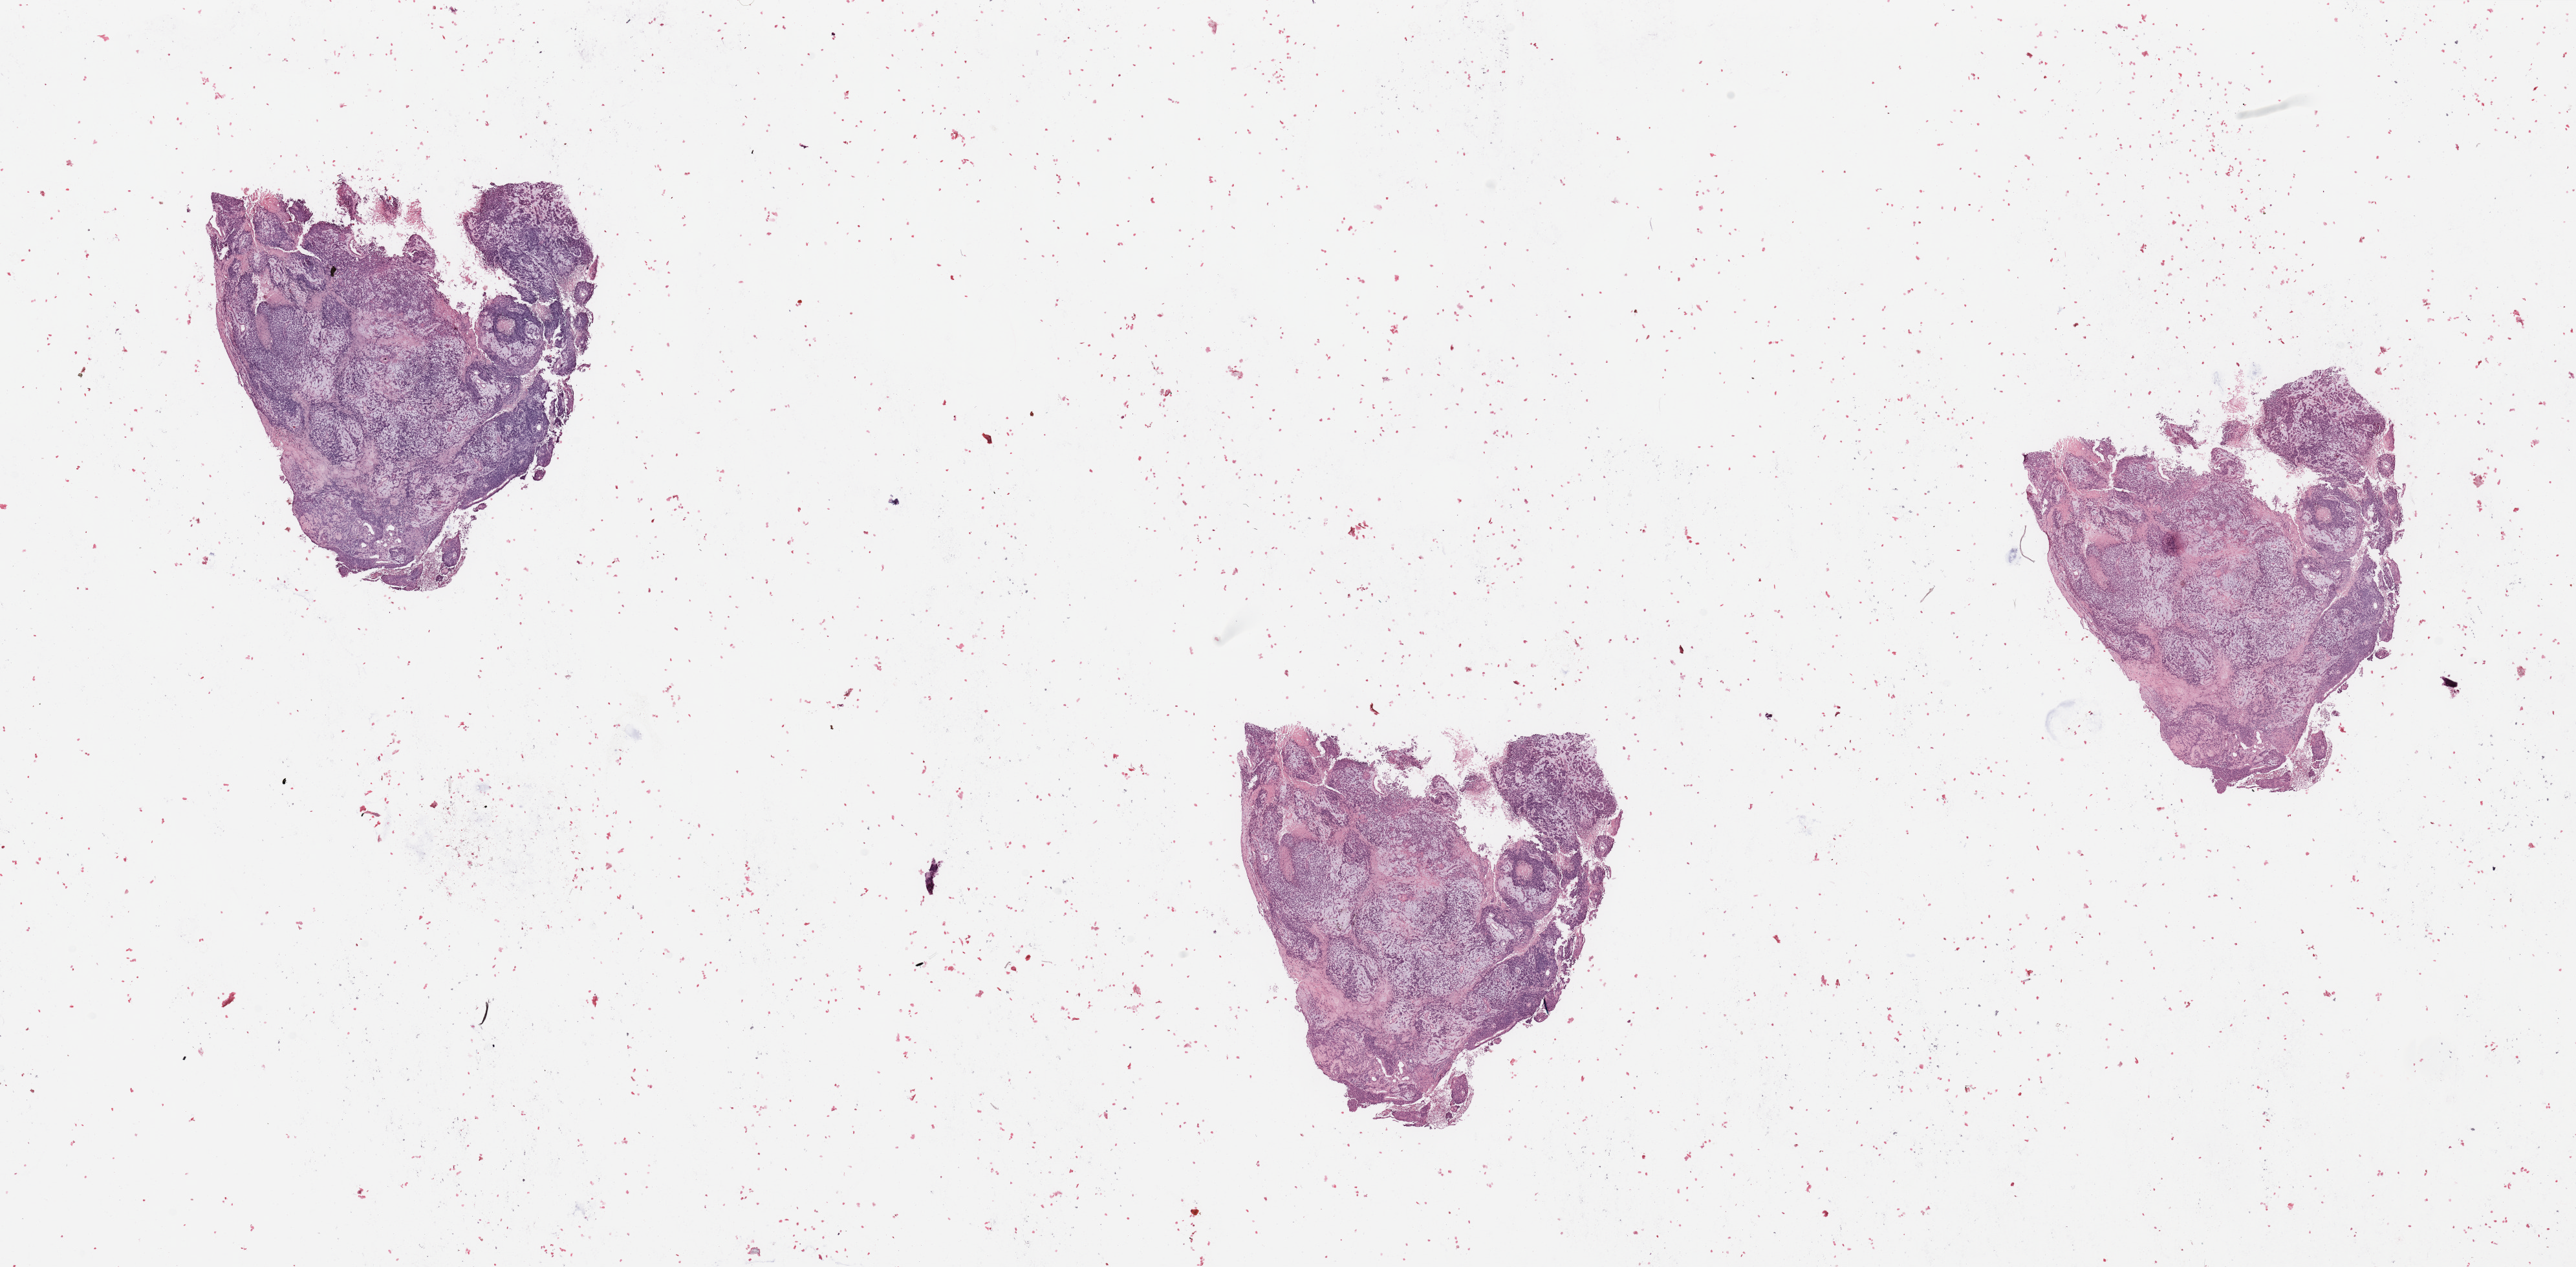
Digitized Hematoxylin and eosin (H&E) stained tissue section (whole slide) — whole scanned area (about 31.5 x 15.5 mm, acquisition: 20x scan) shown as a low-resolution overview; tumour tissue sample, uterus. 59-year-old female patient. Histologic grade: G3 (poorly differentiated).
Primary tumour site (as recorded): anterior endometrium. Histologic diagnosis: Endometrioid adenocarcinoma, NOS. AJCC pathologic stage: I.